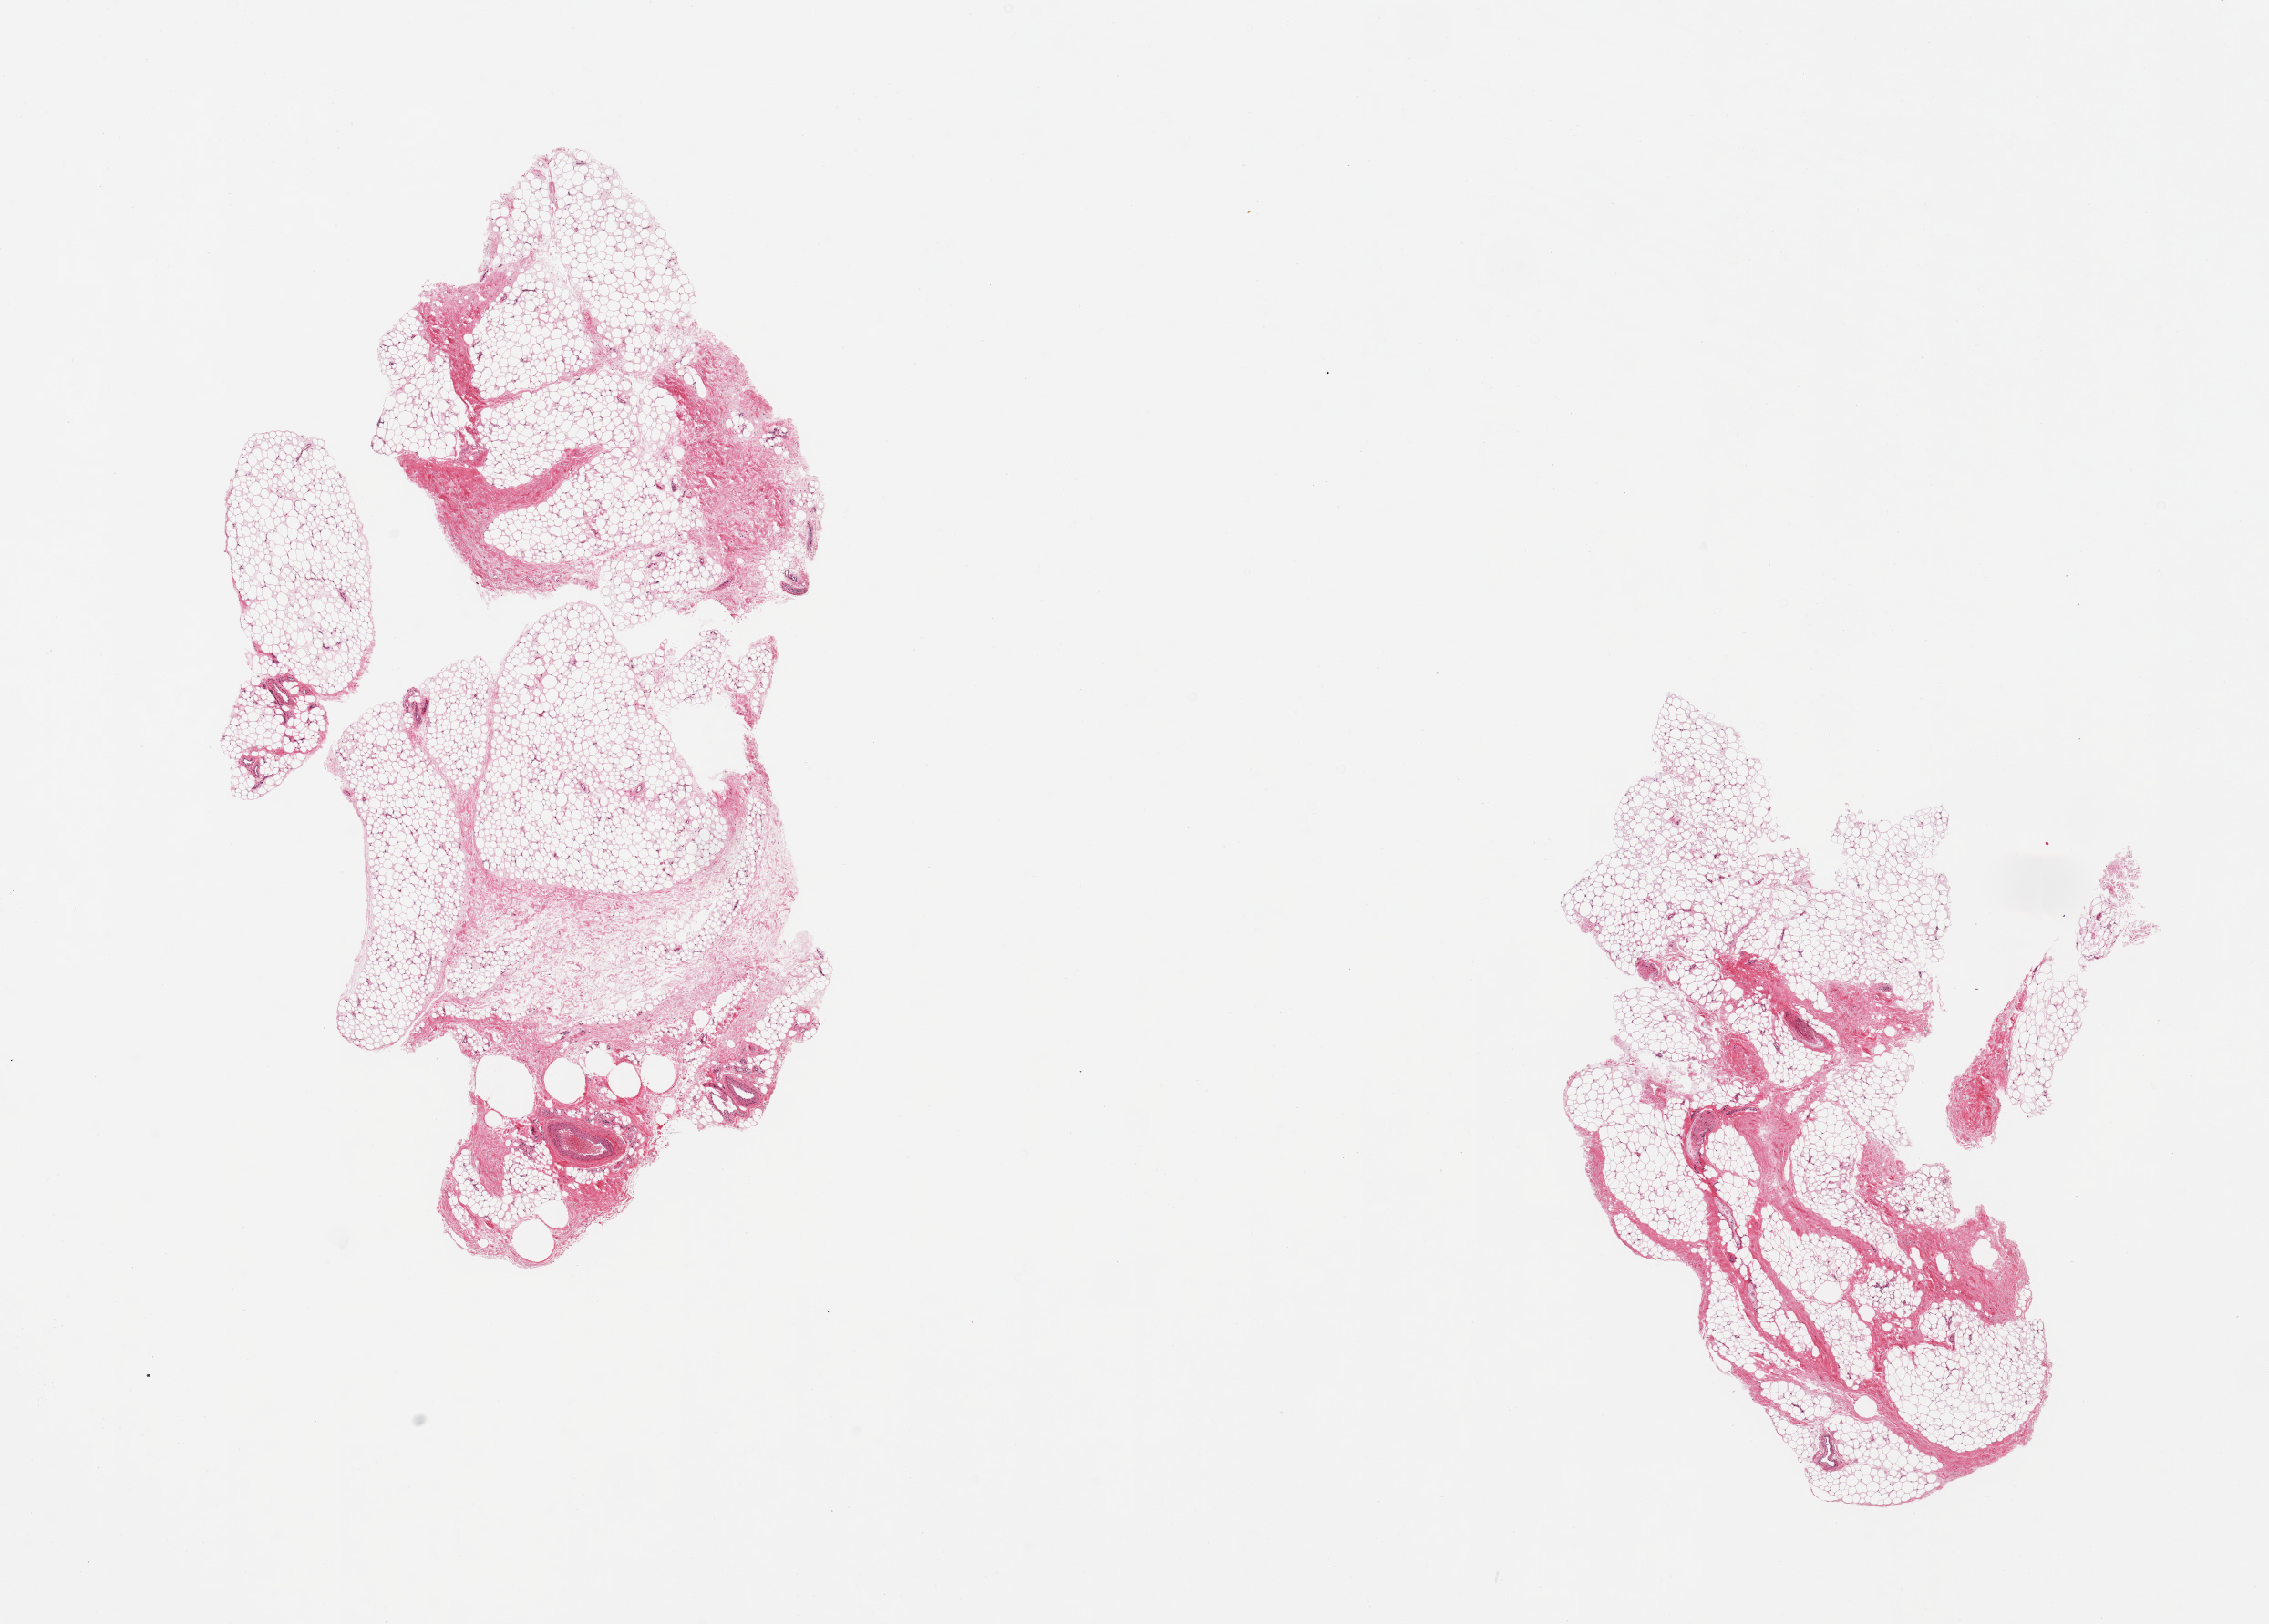
Haematoxylin and eosin whole-slide image, a low-resolution overview of the entire scanned area, about 19.7 x 14.1 mm (from a 20x scan); PAXgene-fixed, paraffin-embedded tissue; target tissue: adipose tissue; tissue donor sample. Male donor.
Pathologist's review note for this sample: 2 pieces; 10% fibrous content.